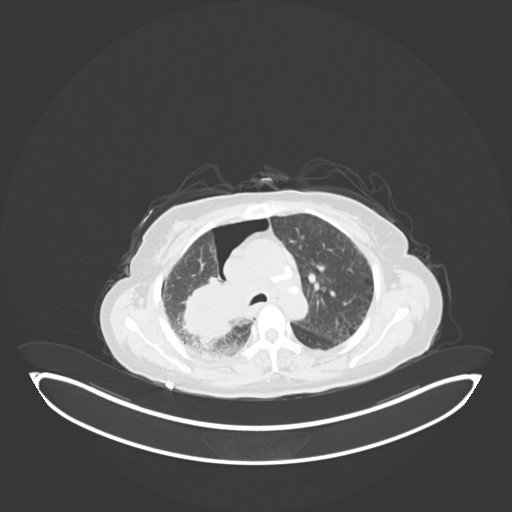
Chest CT, one axial slice. Slice 40 of 69 in the series (ordered by position). Lung window (W 1500 / L -600 HU). 3 mm slice thickness. 512 × 512 image matrix. Female patient, age 64 years. From the clinical record (not read from this slice): clinical TNM (as recorded): T3 N3 M0.
Annotated regions visible in this slice (bounding box drawn by a radiologist):
- lung tumour (recorded histology: squamous cell carcinoma): bounding box [x1, y1, x2, y2] px = [176, 276, 237, 350]